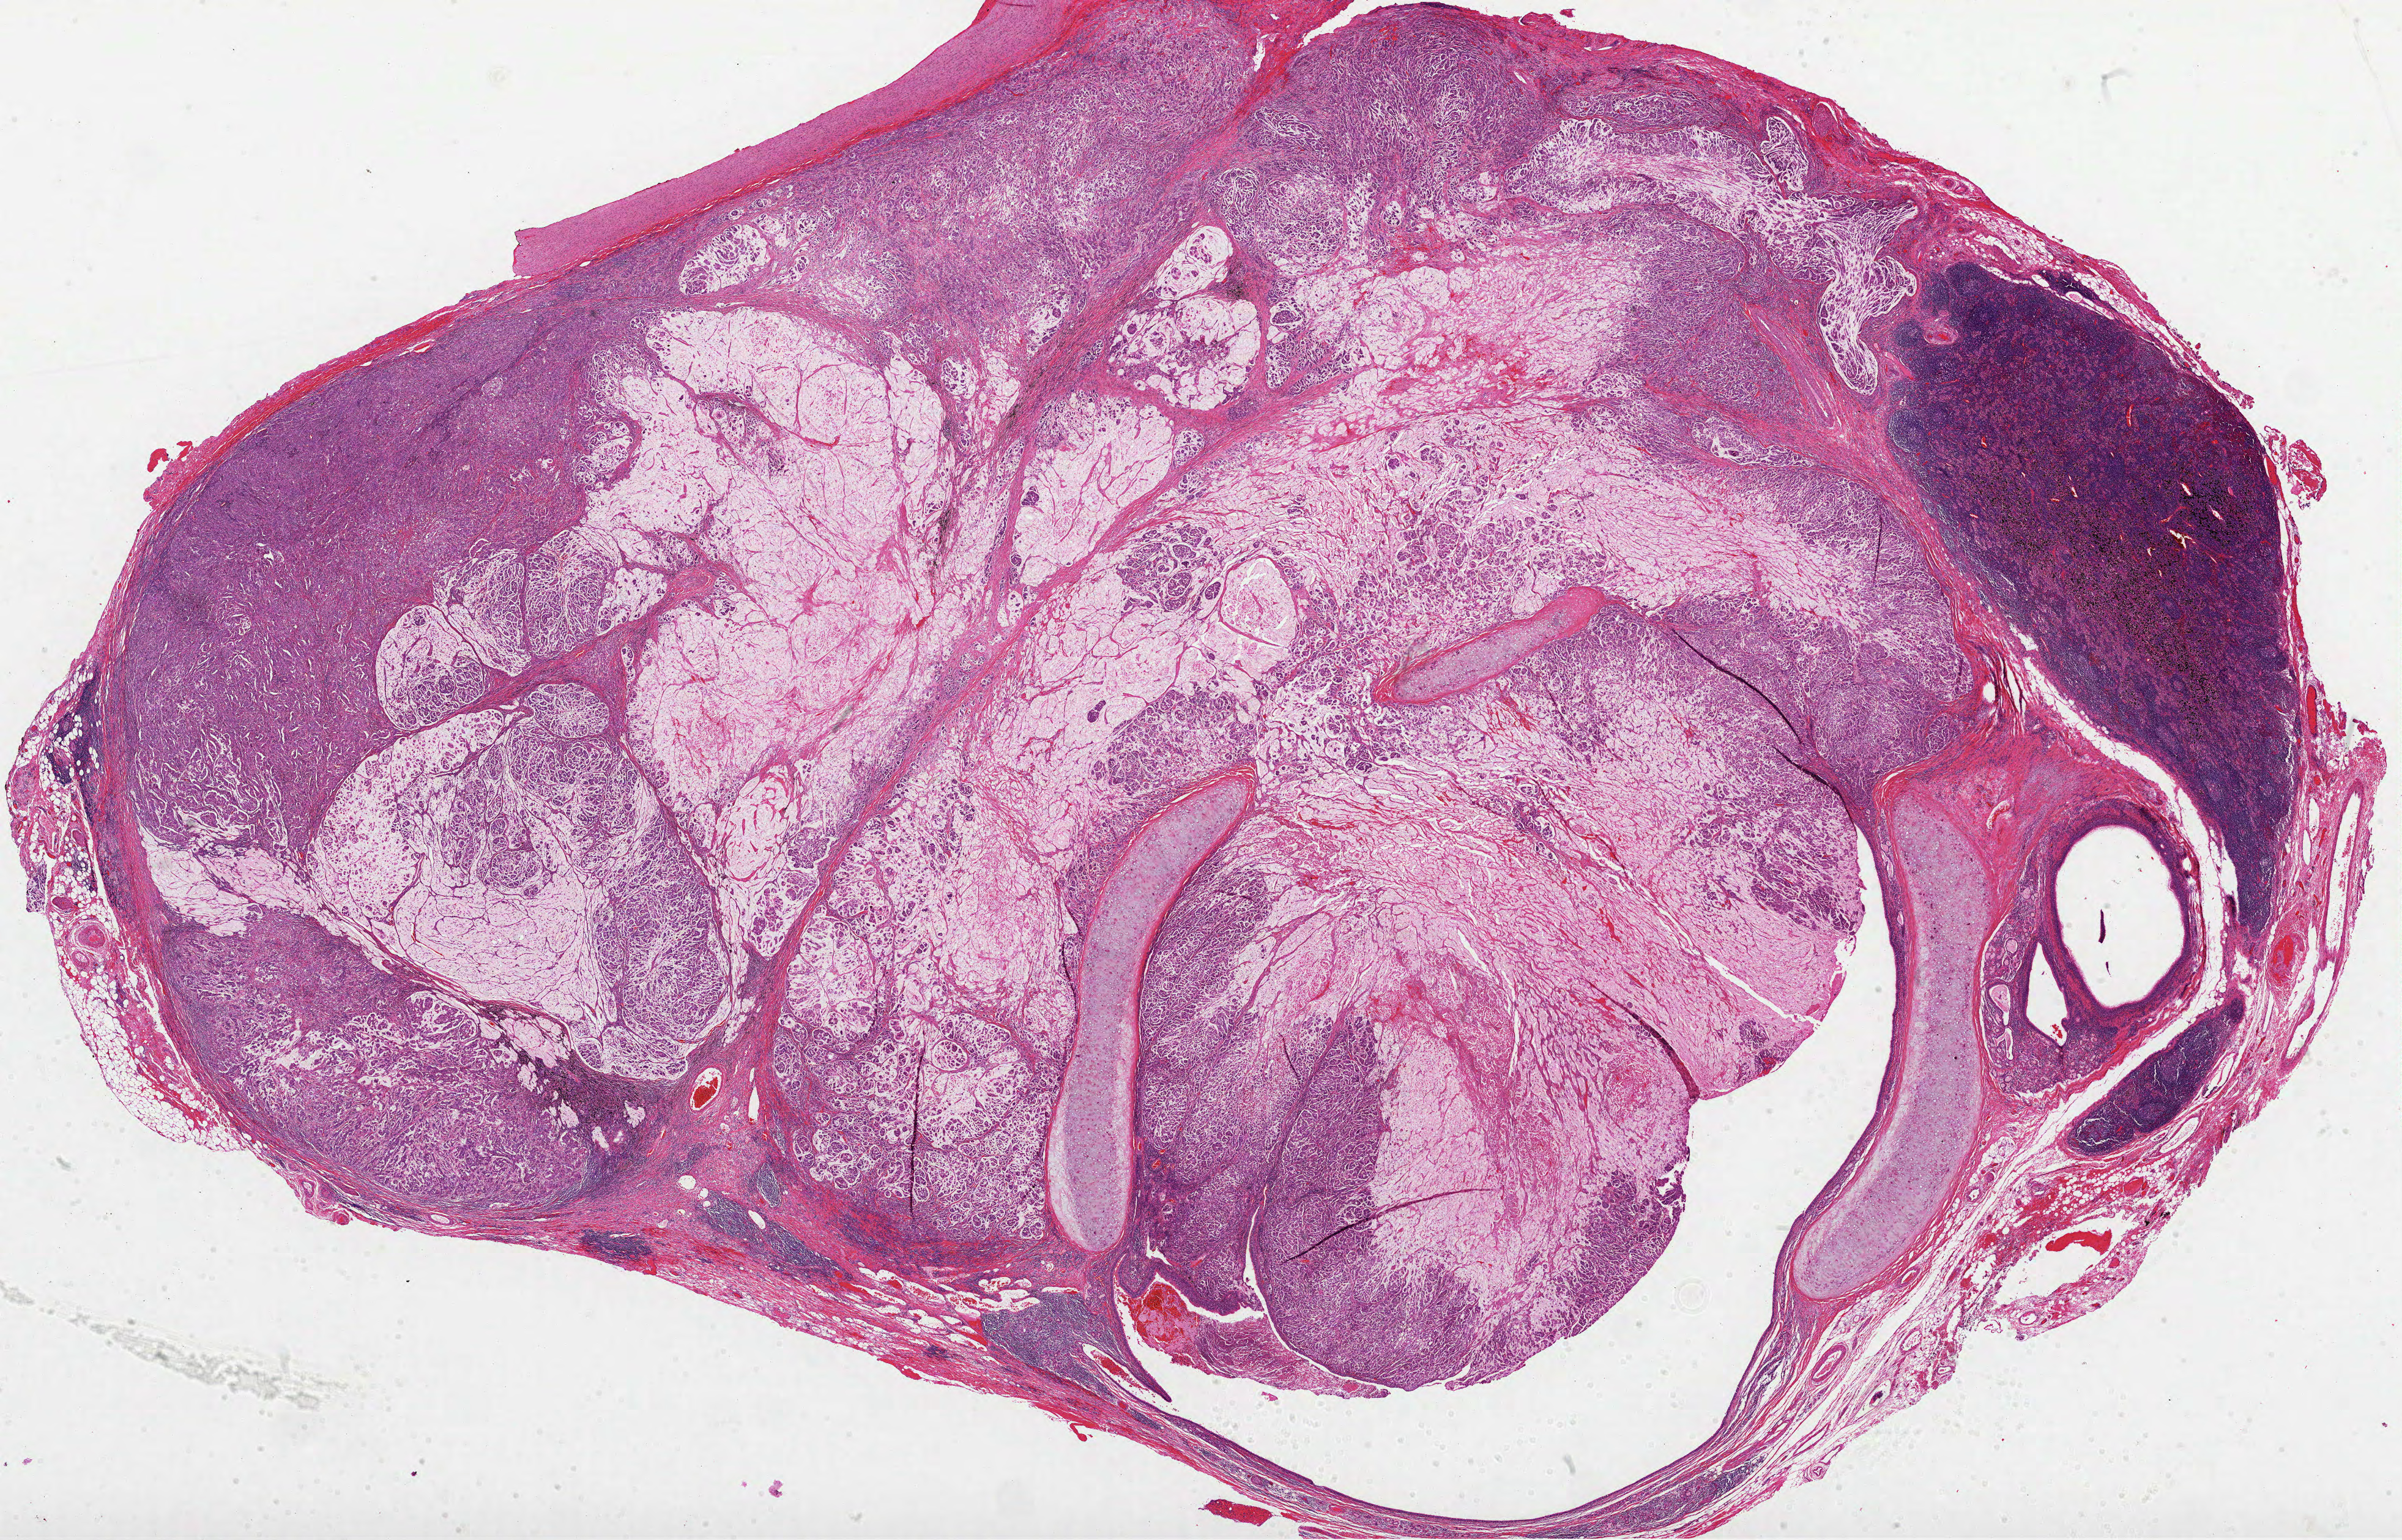
H&E-stained whole-slide image — whole scanned area (about 31.7 x 20.3 mm) shown as a low-resolution overview; FFPE section; lung, primary tumour sample. Female patient; age at initial diagnosis 68 years.
• AJCC pathologic stage: IIB (4th edition)
• histologic diagnosis: Adenocarcinoma, NOS (upper lobe, lung)
• laterality: left